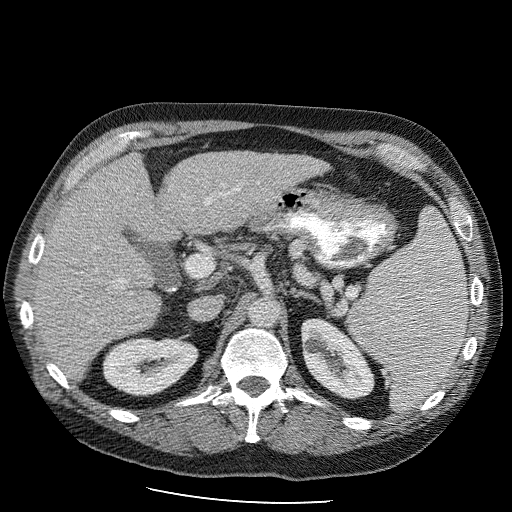
Contrast-enhanced abdominal CT (liver protocol), one axial slice; slice 53 of 98 in the series (ordered by position); 120 kVp; soft-tissue window (W 400 / L 40 HU); 2.5 mm slice thickness; 512 × 512 image matrix, field of view 400 × 400 mm. From the clinical record (not read from this slice): diagnosis: hepatocellular carcinoma (patient treated with transarterial chemoembolisation; whether this scan precedes or follows treatment is not stated here); TNM stage (as recorded): Stage-II; Child-Pugh class: B.
Outlined on this slice (semi-automatically segmented with operator editing):
- liver parenchyma outside the tumour (the mass and vessels are separate outlines, so this box may not span the whole liver): bounding box [x1, y1, x2, y2] px = [32, 150, 329, 378]
- liver vessels: [39, 188, 235, 283]